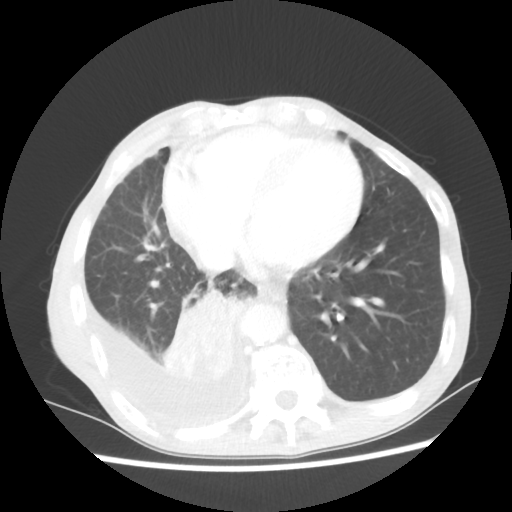
Chest CT, one axial slice. Position 20 of 60 along the scan axis. Reconstruction kernel STANDARD. 80 kVp. Lung window (W 1500 / L -600 HU). 5 mm slice thickness. 512 × 512 image matrix, field of view 335 × 335 mm. Patient: male, 76 years. From the clinical record (not read from this slice): clinical TNM (as recorded): T3 N3 M1a; histopathological grade: G3.
Outlined on this slice (bounding box drawn by a radiologist):
- lung tumour (recorded histology: squamous cell carcinoma): bounding box [x1, y1, x2, y2] px = [161, 283, 251, 385]